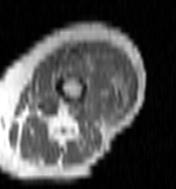
MRI of an extremity soft-tissue mass, one axial slice; position 35 of 100 along the scan axis; MR volume resampled by the dataset authors to the PET/CT grid (not the native acquisition matrix); 3.27 mm slice thickness; 176 × 189 image matrix. Female patient. Case-level facts recorded for this patient, not image findings: histological type: undifferentiated – high grade; grade: high; site of the primary tumour: left thigh.
Annotated regions visible in this slice (expert contour drawn on MRI and transferred to this co-registered scan by the dataset authors):
- gross tumour volume including surrounding oedema: bounding box (x1, y1, x2, y2) in pixels: (62, 52, 125, 117)
- gross tumour volume (mass): (105, 66, 111, 69)